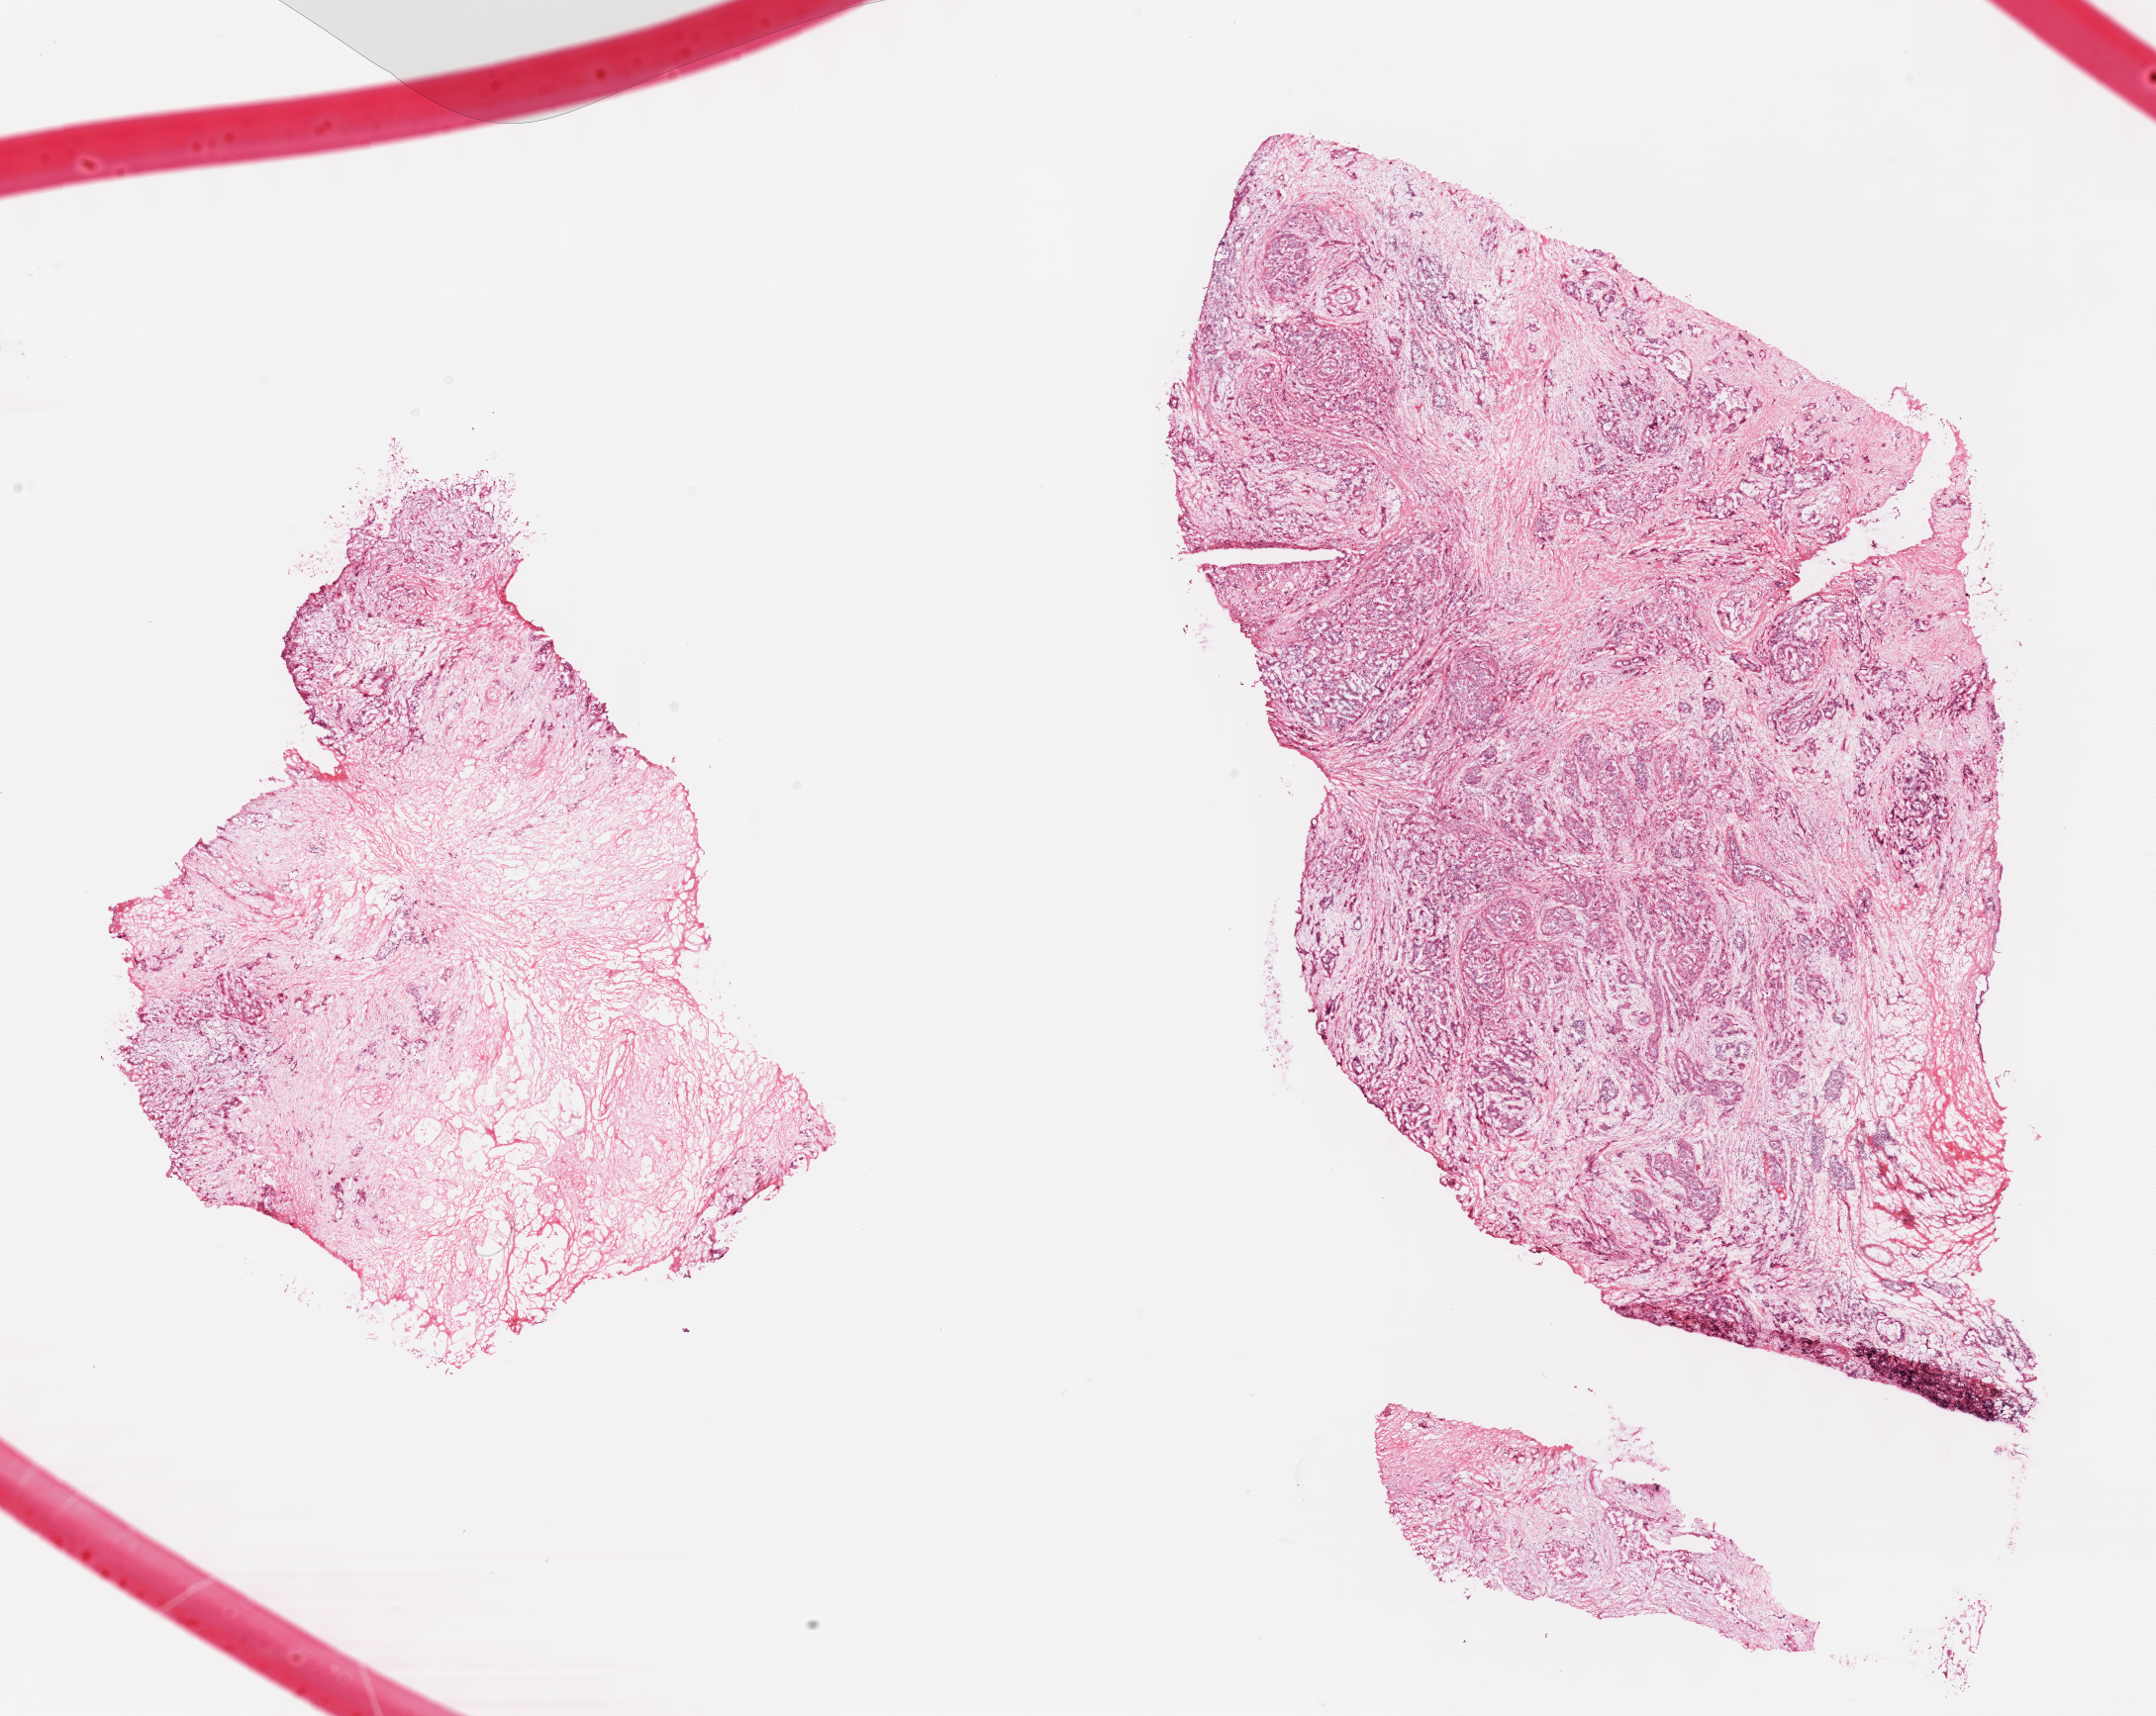
Whole-slide histology image, H&E — whole scanned area (about 17.6 x 14.0 mm, acquisition: 40x scan) shown as a low-resolution overview. Formalin-fixed paraffin-embedded (FFPE) diagnostic section. Pancreas, primary tumour sample. Female, age 80 years at initial diagnosis. Histologic grade: G3 (poorly differentiated).
• AJCC pathologic stage: IIB (7th edition)
• histologic diagnosis: Infiltrating duct carcinoma, NOS (head of pancreas)
• TNM: T3 N1 MX